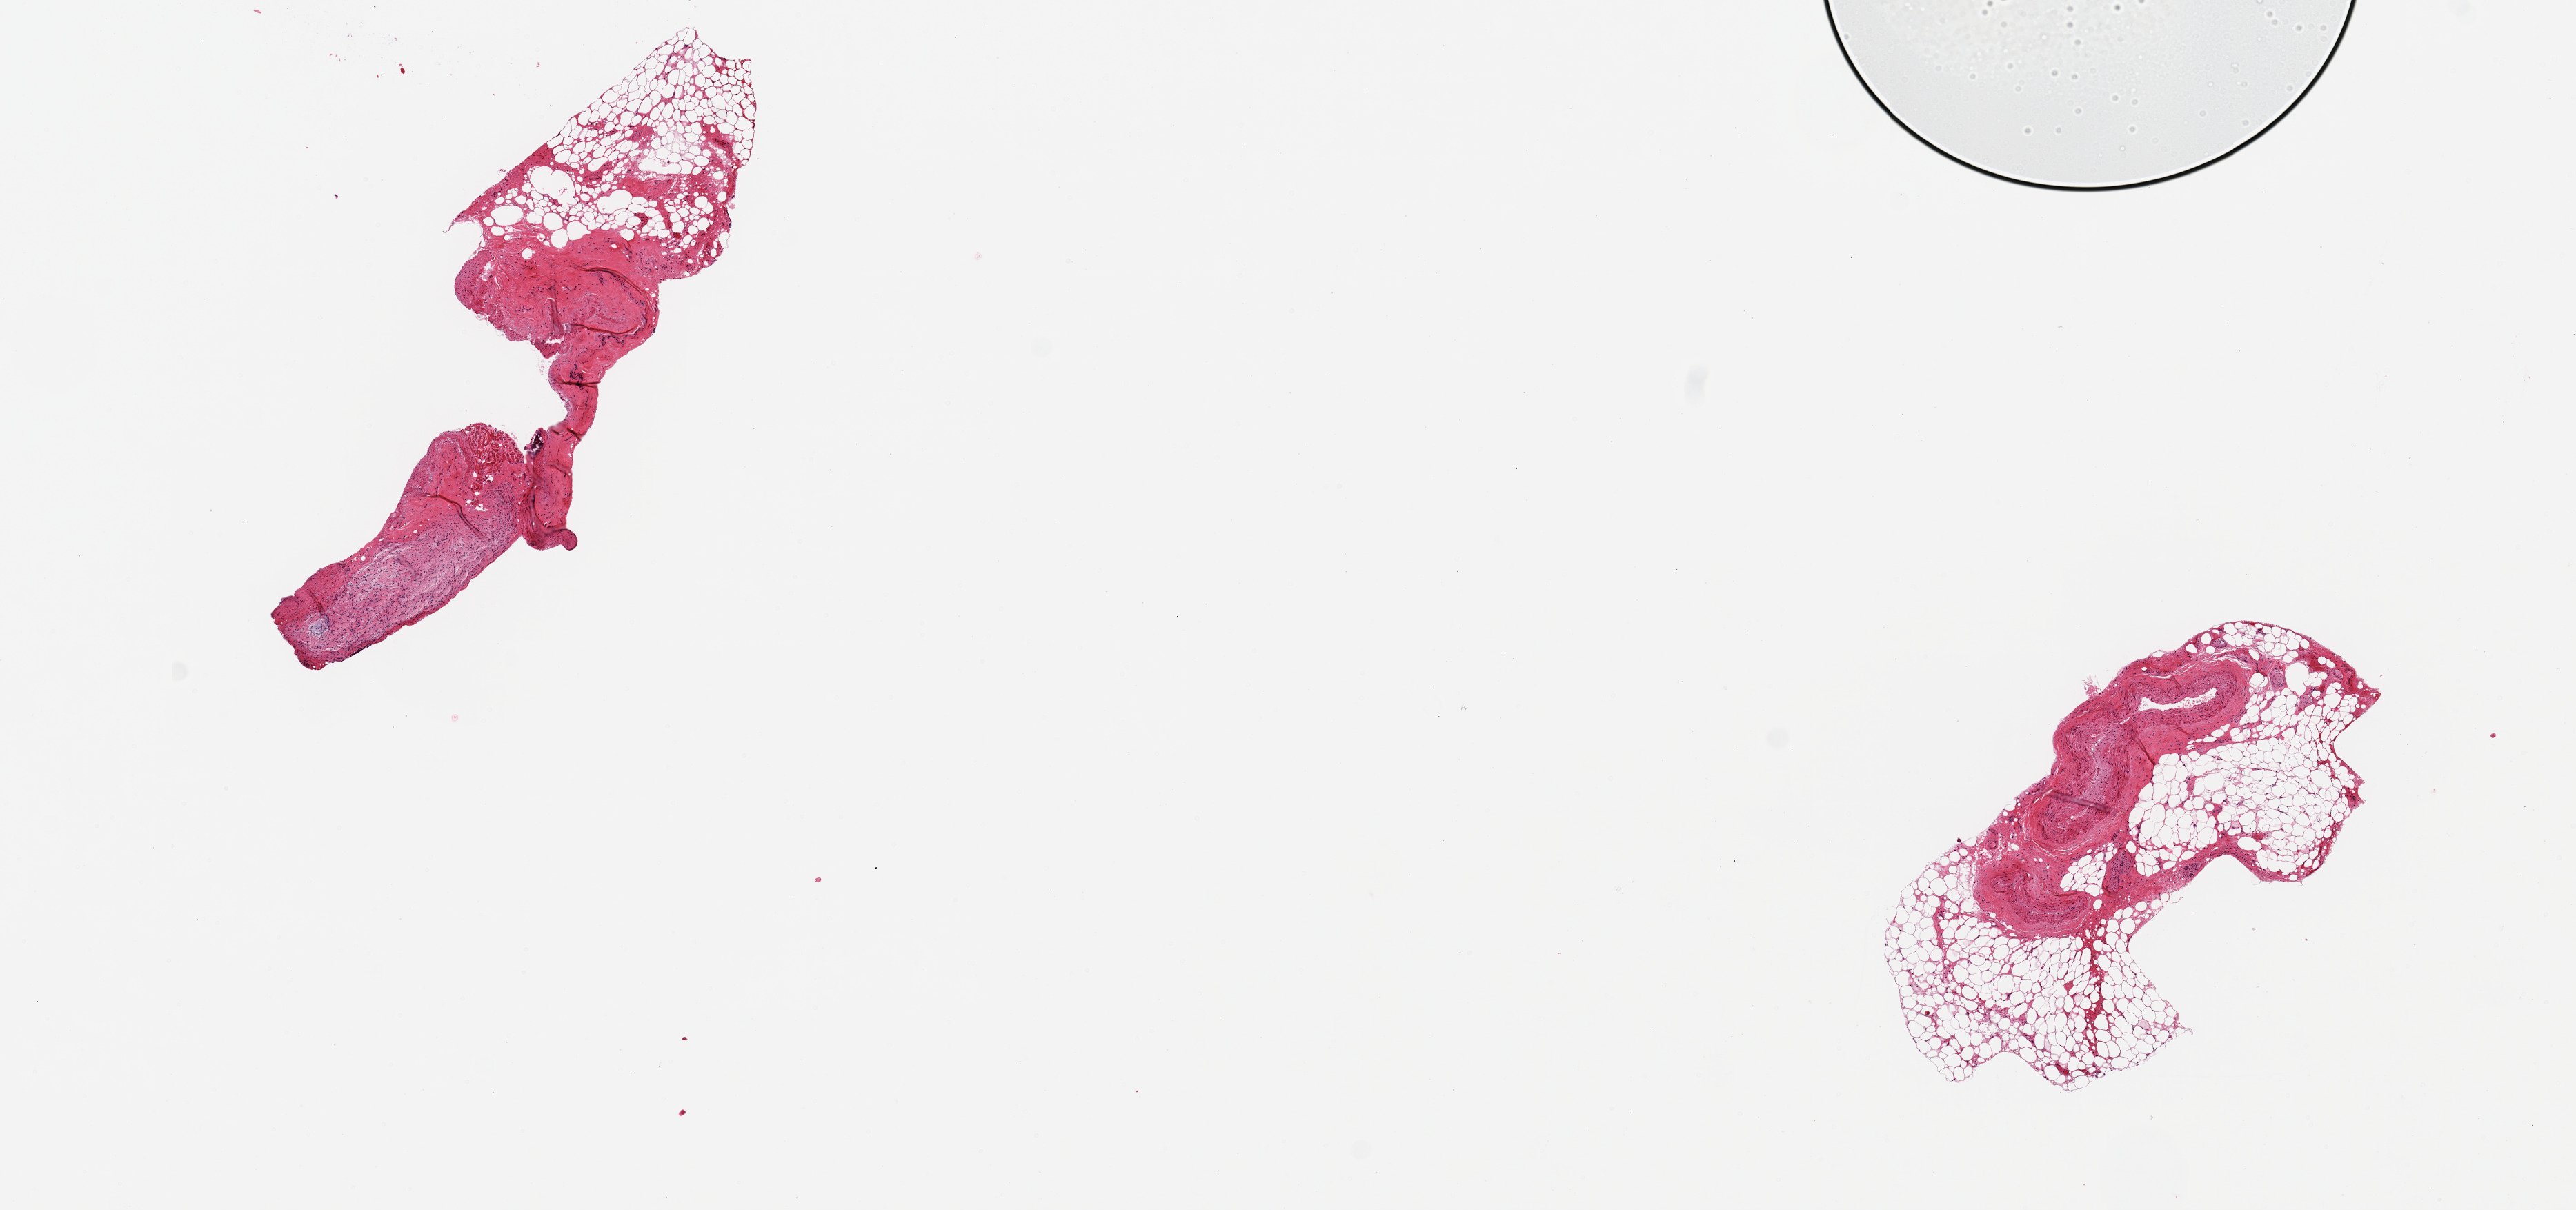
Hematoxylin and eosin (H&E) whole-slide image, brightfield, a low-resolution overview of the entire scanned area, about 14.8 x 6.9 mm. PAXgene-fixed, paraffin-embedded tissue. Sampled site (target tissue): coronary artery. Donor tissue sample. Male donor.
* reviewer comment on this tissue sample: 2 pieces, 4x1 & 3x2mm; Sclerotic vessels. 60% extraneous adipose